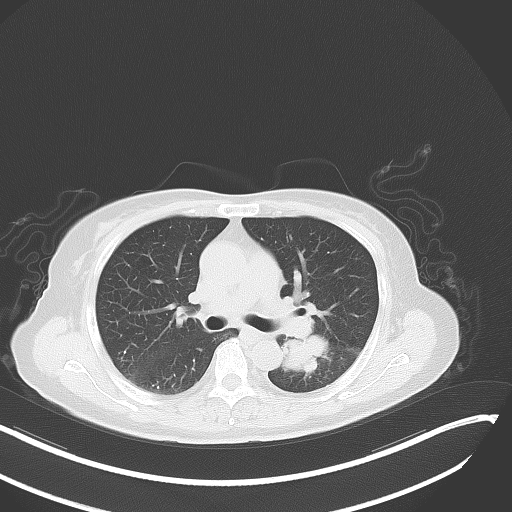
Chest CT, one axial slice; position 24 of 48 along the scan axis; reconstruction kernel B70f; 120 kVp; lung window (W 1500 / L -600 HU); 5 mm slice thickness; 512 × 512 image matrix, field of view 400 × 400 mm. Patient: female, 64 years. From the clinical record (not read from this slice): clinical TNM (as recorded): T3 N1 M1.
Annotated regions visible in this slice (bounding box drawn by a radiologist):
- lung tumour (recorded histology: small cell carcinoma): box from (x=281, y=327) to (x=334, y=376) px